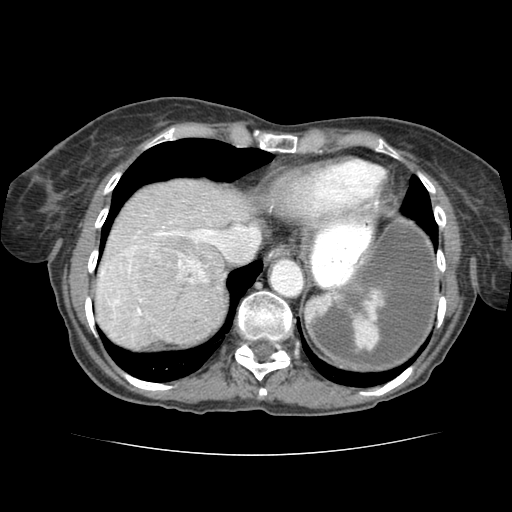
Contrast-enhanced abdominal CT (liver protocol), one axial slice; slice 68 of 77 in the series (ordered by position); reconstruction kernel STANDARD; 120 kVp; soft-tissue window (W 400 / L 40 HU); 2.5 mm slice thickness; 512 × 512 image matrix, field of view 340 × 340 mm. Case-level facts recorded for this patient, not image findings: diagnosis: hepatocellular carcinoma (patient treated with transarterial chemoembolisation; whether this scan precedes or follows treatment is not stated here); TNM stage (as recorded): Stage-I; Child-Pugh class: A; tumour differentiation: well differentiated.
Outlined on this slice (semi-automatically segmented with operator editing):
- abdominal aorta: bounding box <270,259,302,296> (left, top, right, bottom; pixels)
- liver parenchyma outside the tumour (the mass and vessels are separate outlines, so this box may not span the whole liver): <96,178,264,334>
- mass: <135,249,210,338>
- liver vessels: <193,264,218,323>